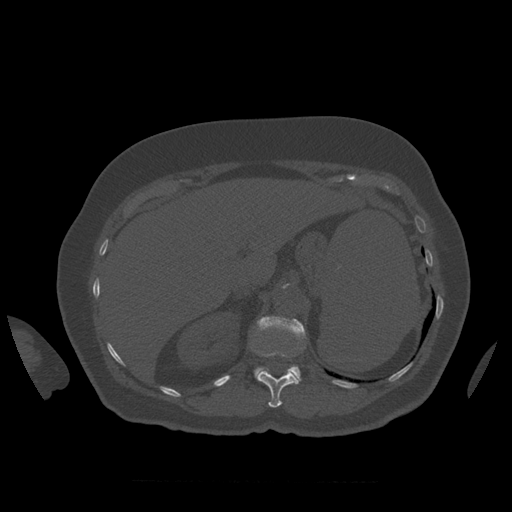
CT including the spine, one axial slice. Slice 293 of 399 in the series (ordered by position). Reconstruction kernel STANDARD. 120 kVp. Bone window (W 1800 / L 400 HU). 1.25 mm slice thickness. 512 × 512 image matrix, field of view 404 × 404 mm. Patient age 81 years. From the clinical record (not read from this slice): primary cancer: renal.
Structures marked on this image (semi-automatic segmentation, software-assisted and operator-edited):
- L1 vertebra: box from (x=254, y=317) to (x=306, y=385) px
- T12 vertebra: (x=257, y=352)–(x=299, y=408)